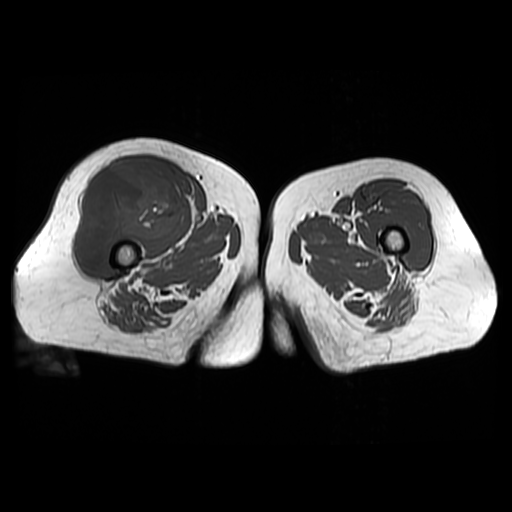
MRI of an extremity soft-tissue mass, one axial slice. Position 32 of 48 along the scan axis. 6 mm slice thickness. 512 × 512 image matrix, field of view 440 × 440 mm. Female patient. Case-level facts recorded for this patient, not image findings: histological type: pleiomorphic undifferentiated sarcoma; grade: high; site of the primary tumour: right quadricep.
Structures marked on this image (outlined manually by an expert reader):
- gross tumour volume including surrounding oedema: bounding box <74,162,186,267> (left, top, right, bottom; pixels)
- gross tumour volume (mass): <74,162,186,267>